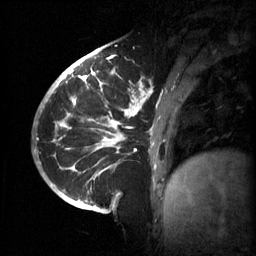
Breast MRI (dynamic contrast-enhanced), one sagittal slice; 3 images stored at this slice position (order not interpretable as contrast timing); 1.5 T; TE 4.2 ms, TR 11 ms; 2 mm slice thickness; 256 × 256 image matrix, field of view 220 × 220 mm. Patient: female, 51 years.
Outlined on this slice (semi-automatically segmented with operator editing):
- analysis volume of interest (the breast-tissue region the enhancement analysis was run in; not a lesion): bounding box [x1, y1, x2, y2] px = [63, 80, 187, 201]
- tumour enhancement mask (voxels above the 70 % enhancement threshold inside the analysis volume of interest): [65, 80, 155, 181]